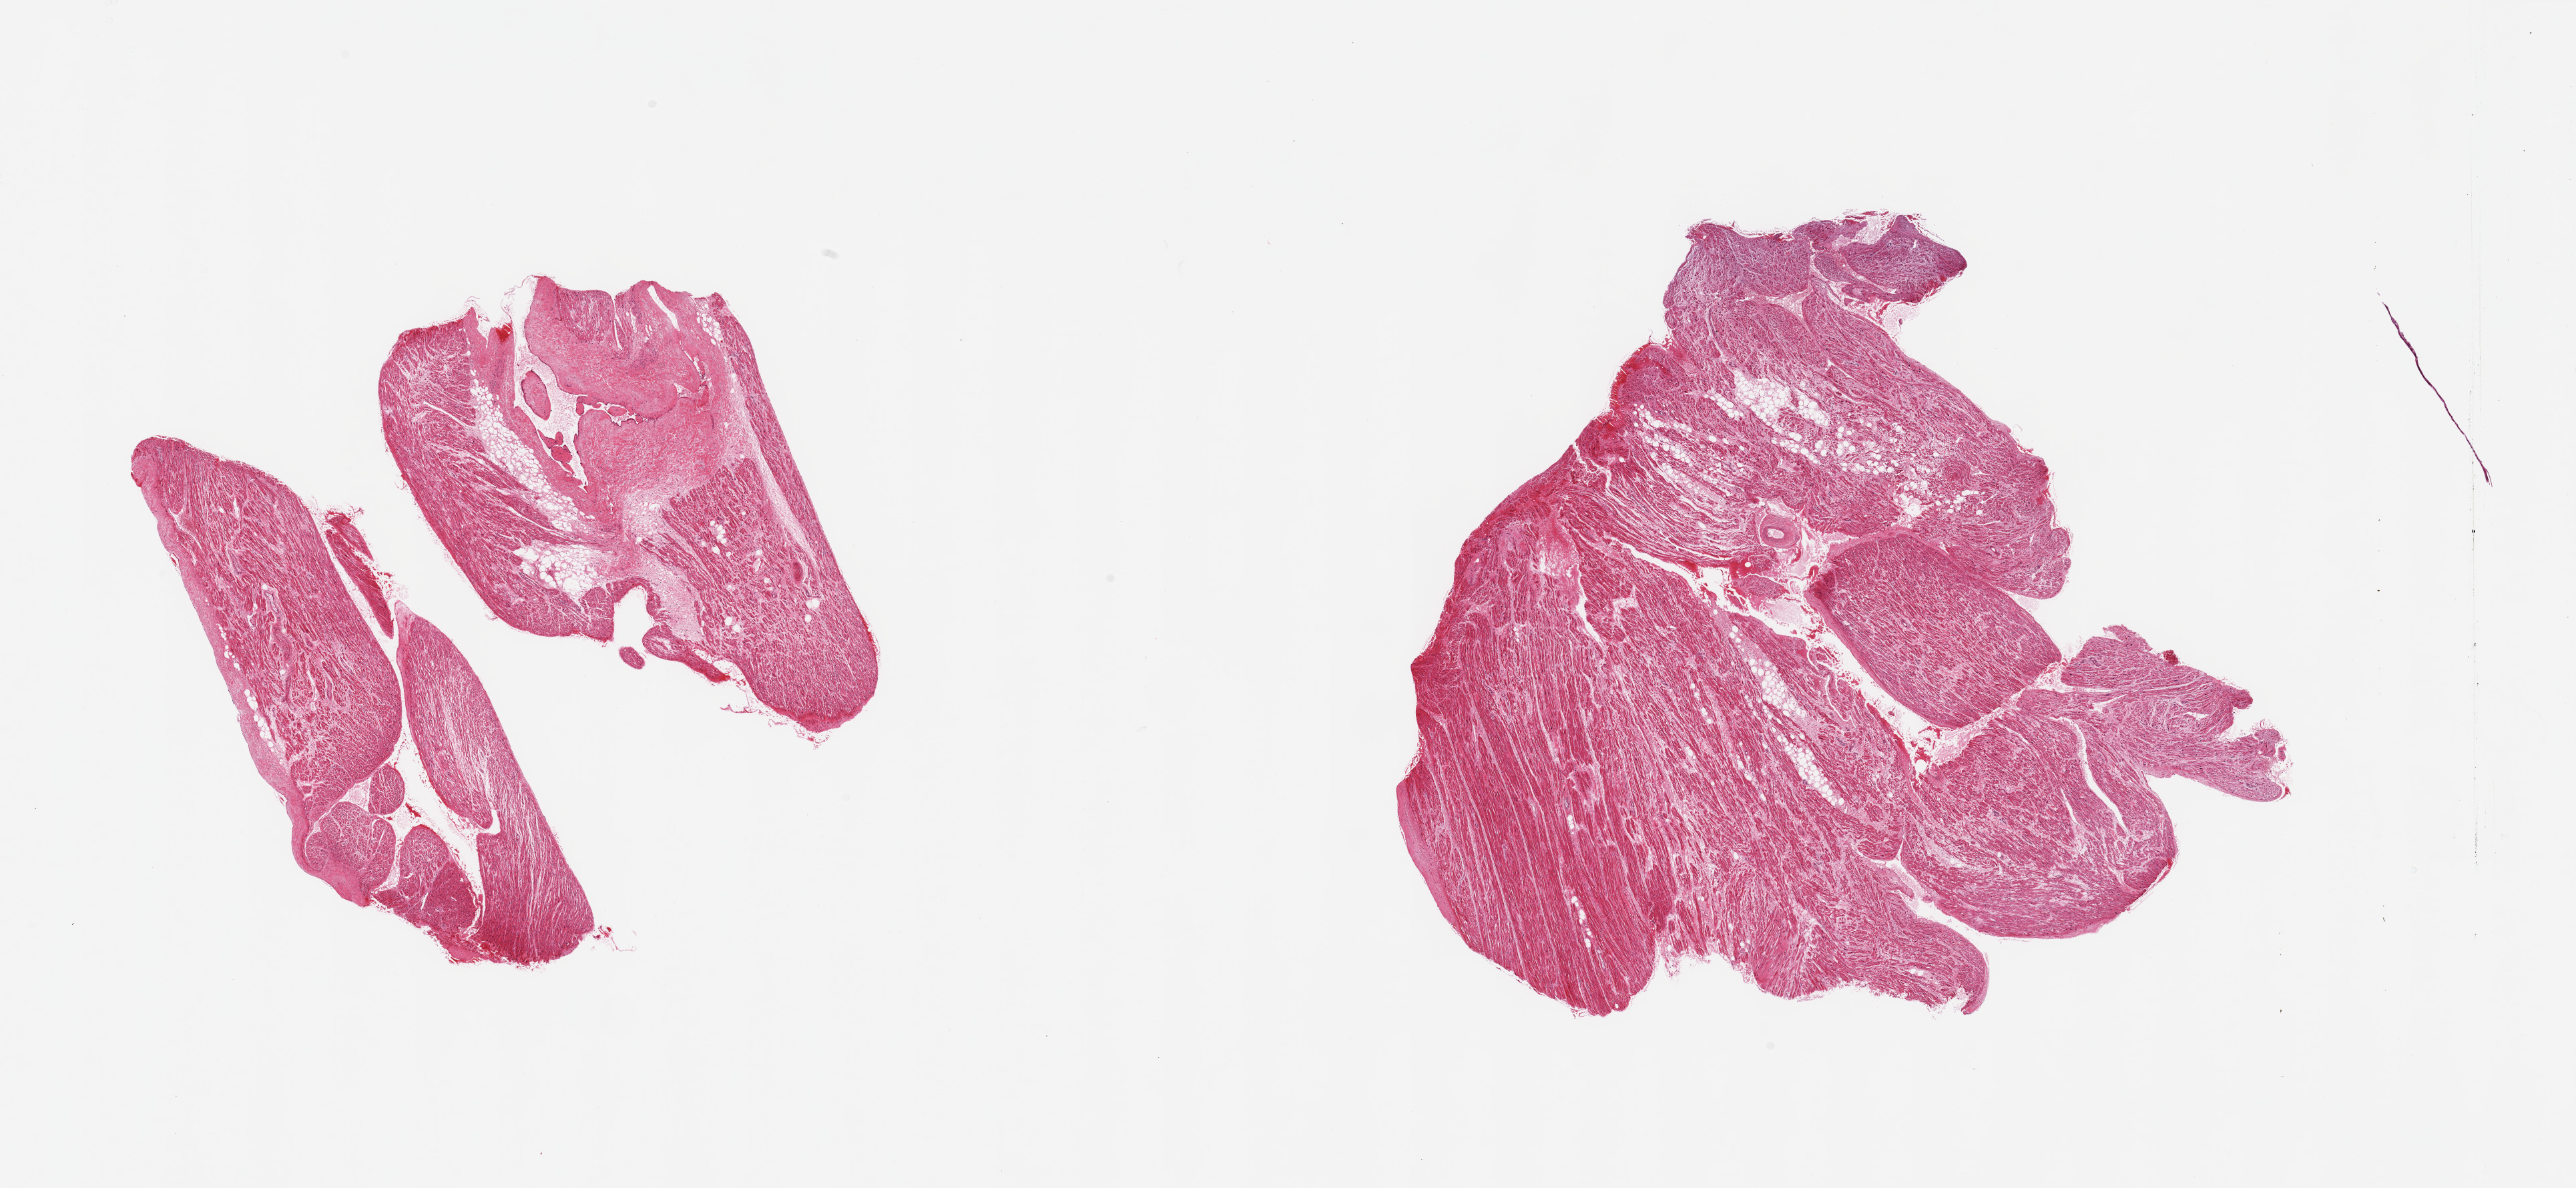
Hematoxylin and eosin (H&E) whole-slide image, brightfield — whole scanned area (about 30.5 x 14.1 mm, acquisition: 20x scan) shown as a low-resolution overview. PAXgene-fixed, paraffin-embedded tissue. Target tissue: auricular appendage. Tissue donor sample. Donor: female.
Pathologist's review note for this sample: 3 pieces; 1 has 40% fibrofatty content.